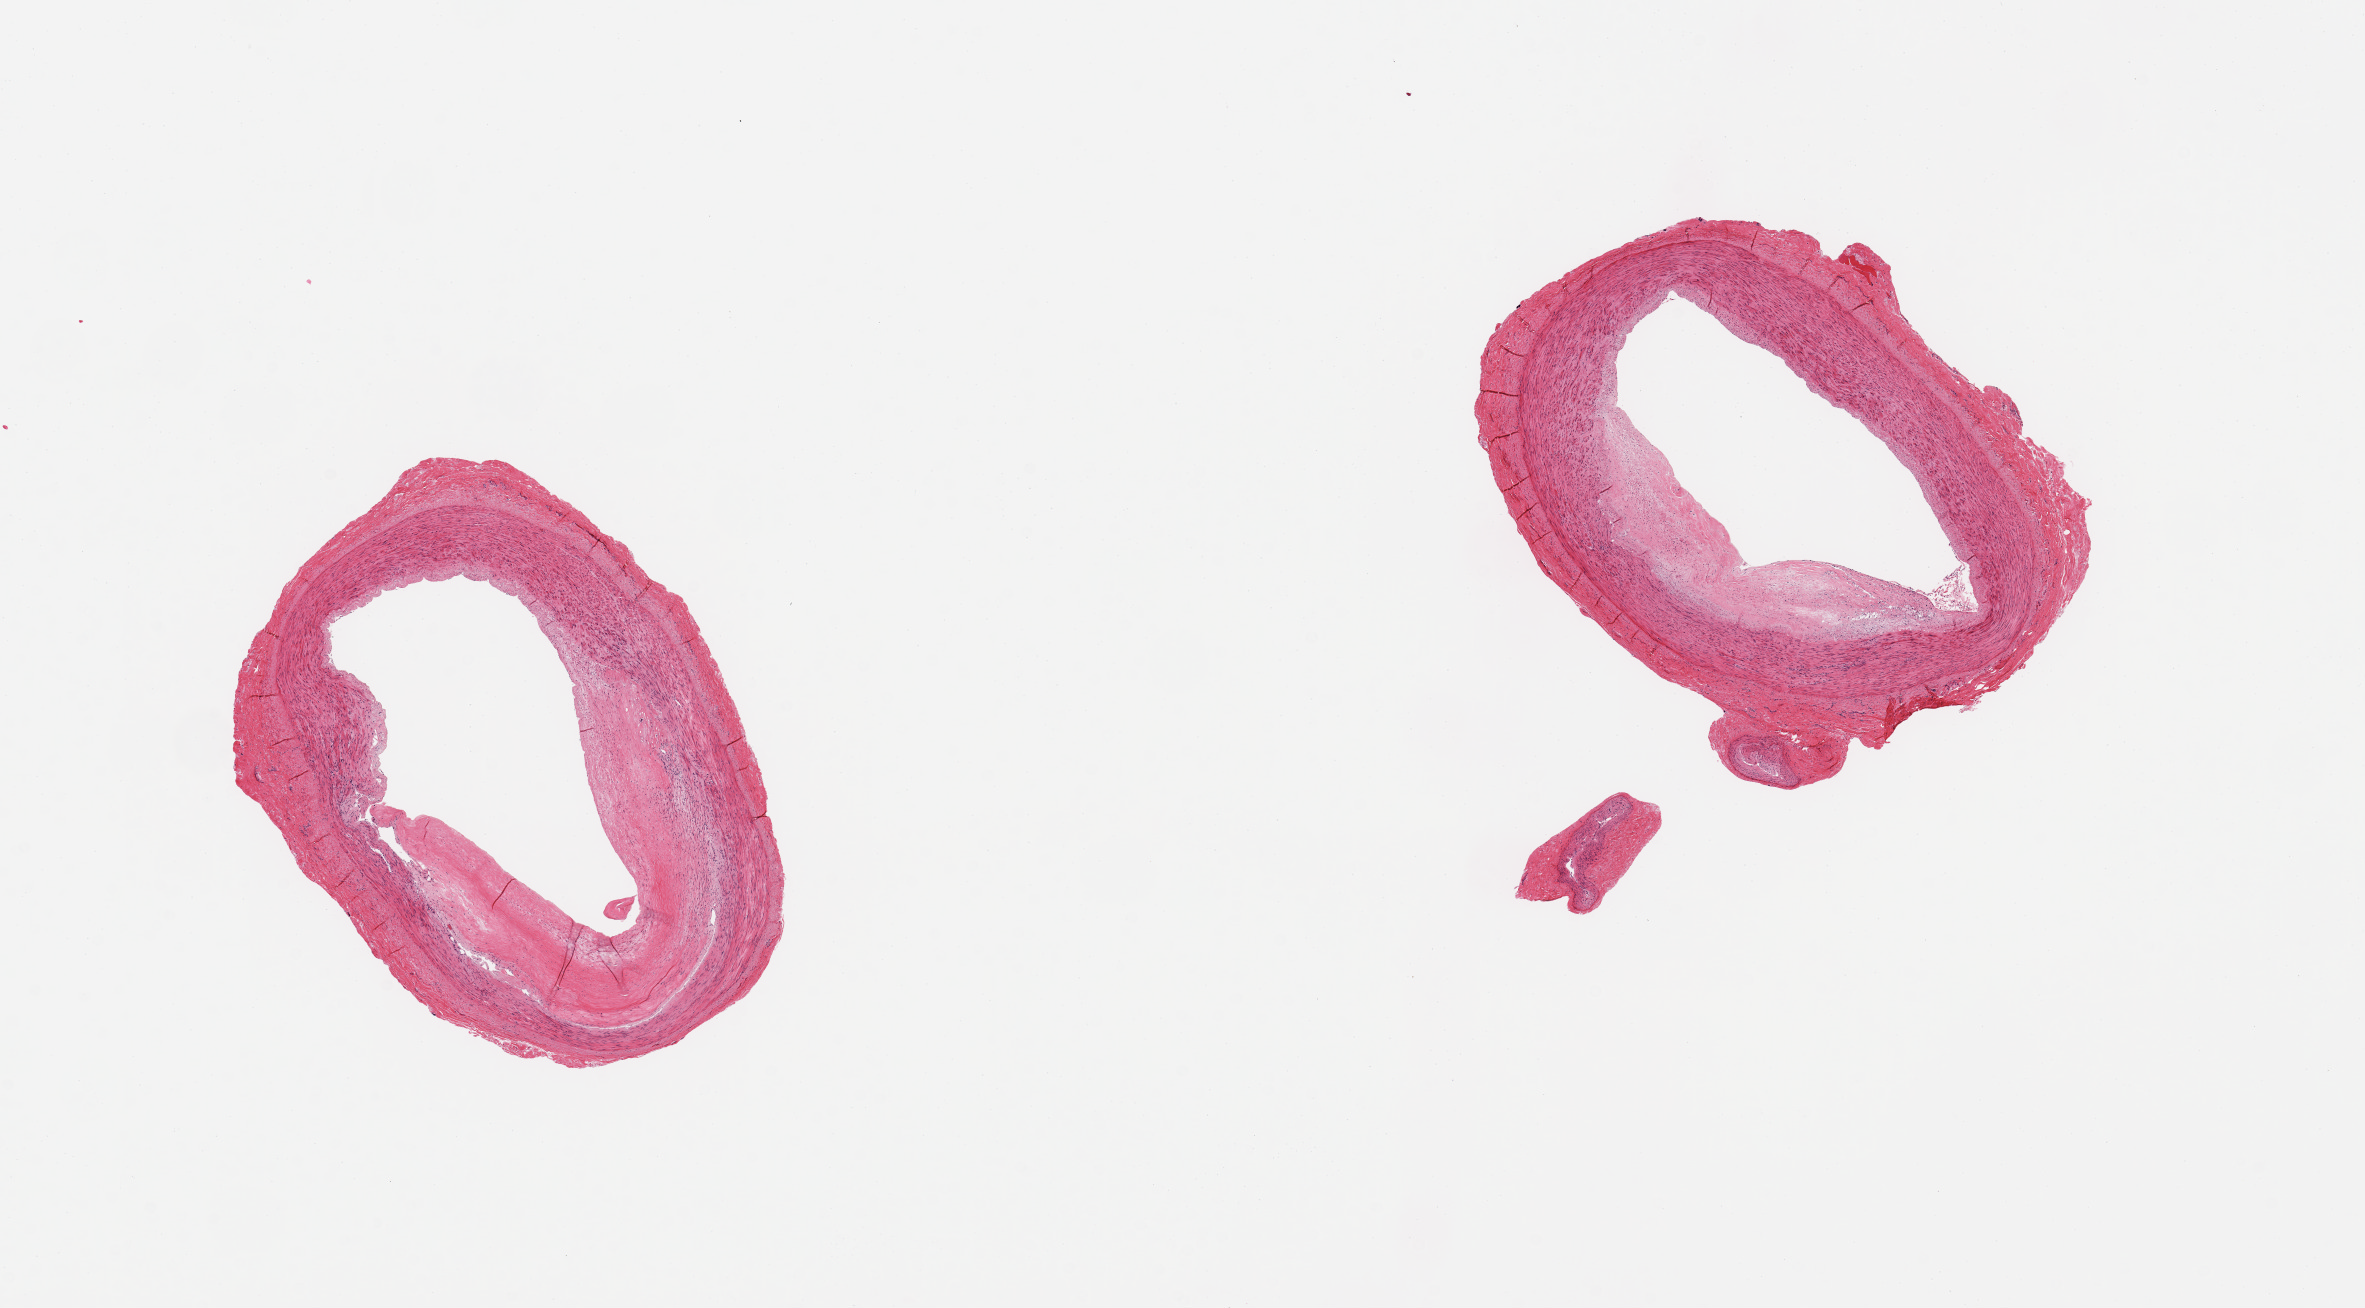
Digitized hematoxylin and eosin (H&E)-stained section — low-resolution overview of the scanned area, about 18.7 x 10.3 mm. PAXgene-fixed, paraffin-embedded tissue. Target tissue: tibial artery. Tissue donor sample. Male donor.
Review note (as recorded): 2 pieces; moderate plaque with widely patent lumen; well trimmed.